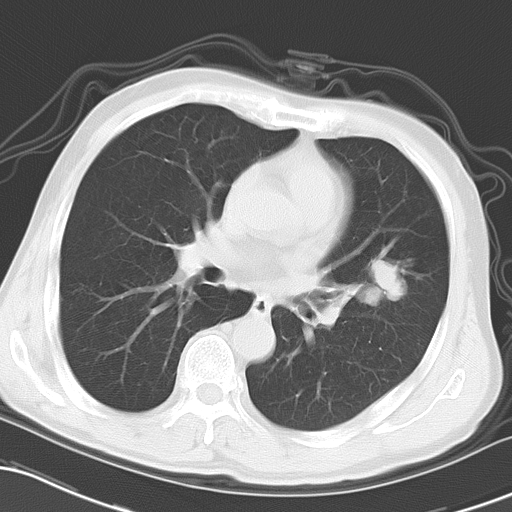
Chest CT, one axial slice; position 14 of 27 along the scan axis; reconstruction kernel B70f; lung window (W 1500 / L -600 HU); 10 mm slice thickness; 512 × 512 image matrix, field of view 318 × 318 mm. Male patient, age 60 years. From the clinical record (not read from this slice): clinical TNM (as recorded): T1c N1 M0; histopathological grade: G3.
Outlined on this slice (rectangle marked by the reading radiologist):
- lung tumour (recorded histology: adenocarcinoma): box from (x=363, y=252) to (x=414, y=312) px
- lung tumour (recorded histology: adenocarcinoma): (x=363, y=253)–(x=416, y=309)